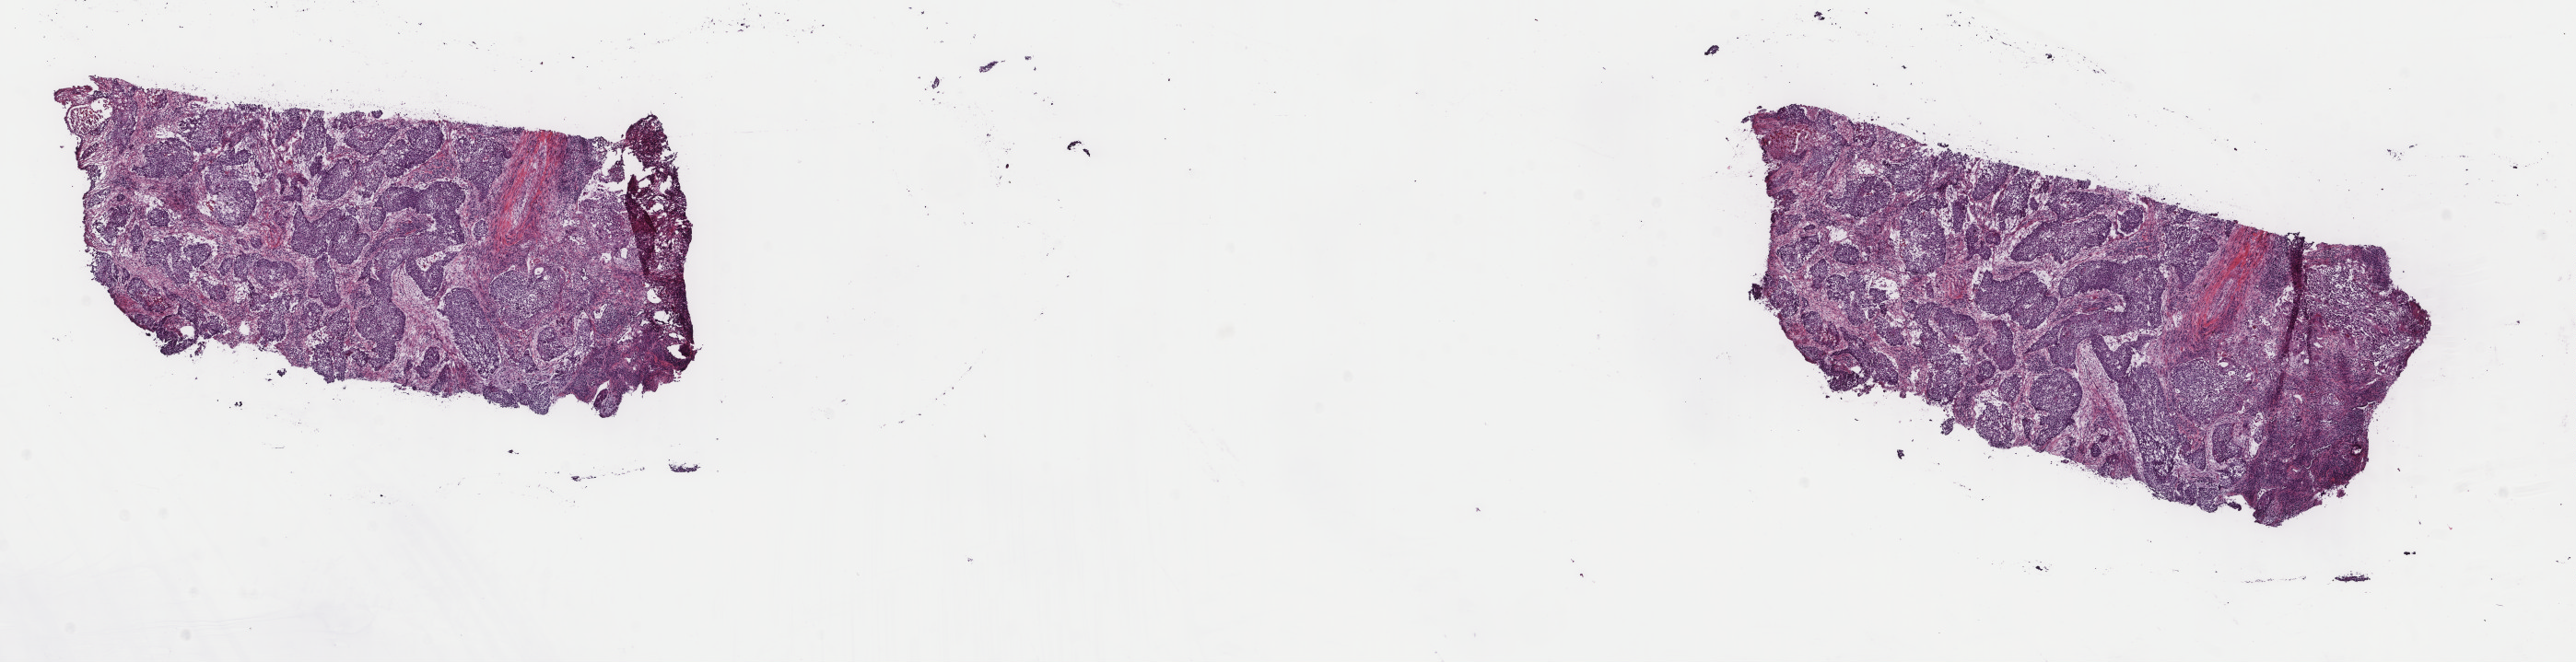
Digitized H&E-stained tissue section (whole slide) — shown as a low-resolution overview of the whole scanned area (about 22.2 x 5.7 mm), frozen section from the top of the tissue portion, primary tumour sample from the lung. Male patient; age at initial diagnosis 61 years.
Pathologic diagnosis: Squamous cell carcinoma, NOS (middle lobe, lung).